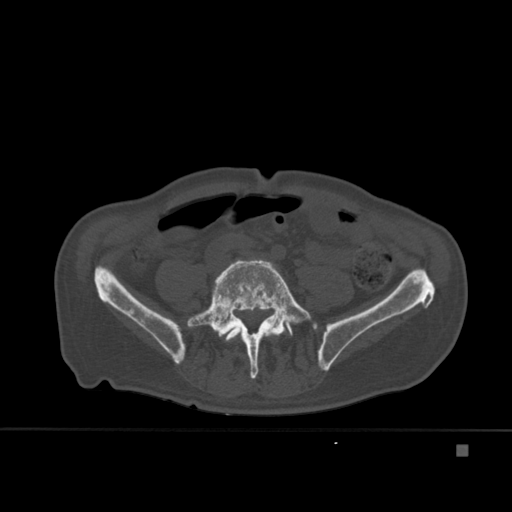
CT including the spine, one axial slice. Position 106 of 451 along the scan axis. Bone window (W 1800 / L 400 HU). 1.5 mm slice thickness. 512 × 512 image matrix. Patient: male, 75 years. From the clinical record (not read from this slice): primary cancer: prostate.
Annotated regions visible in this slice (semi-automatic segmentation, software-assisted and operator-edited):
- L4 vertebra: bounding box [x1, y1, x2, y2] px = [224, 327, 238, 342]
- L5 vertebra: [187, 259, 311, 379]
- T7 vertebra: [215, 301, 270, 326]